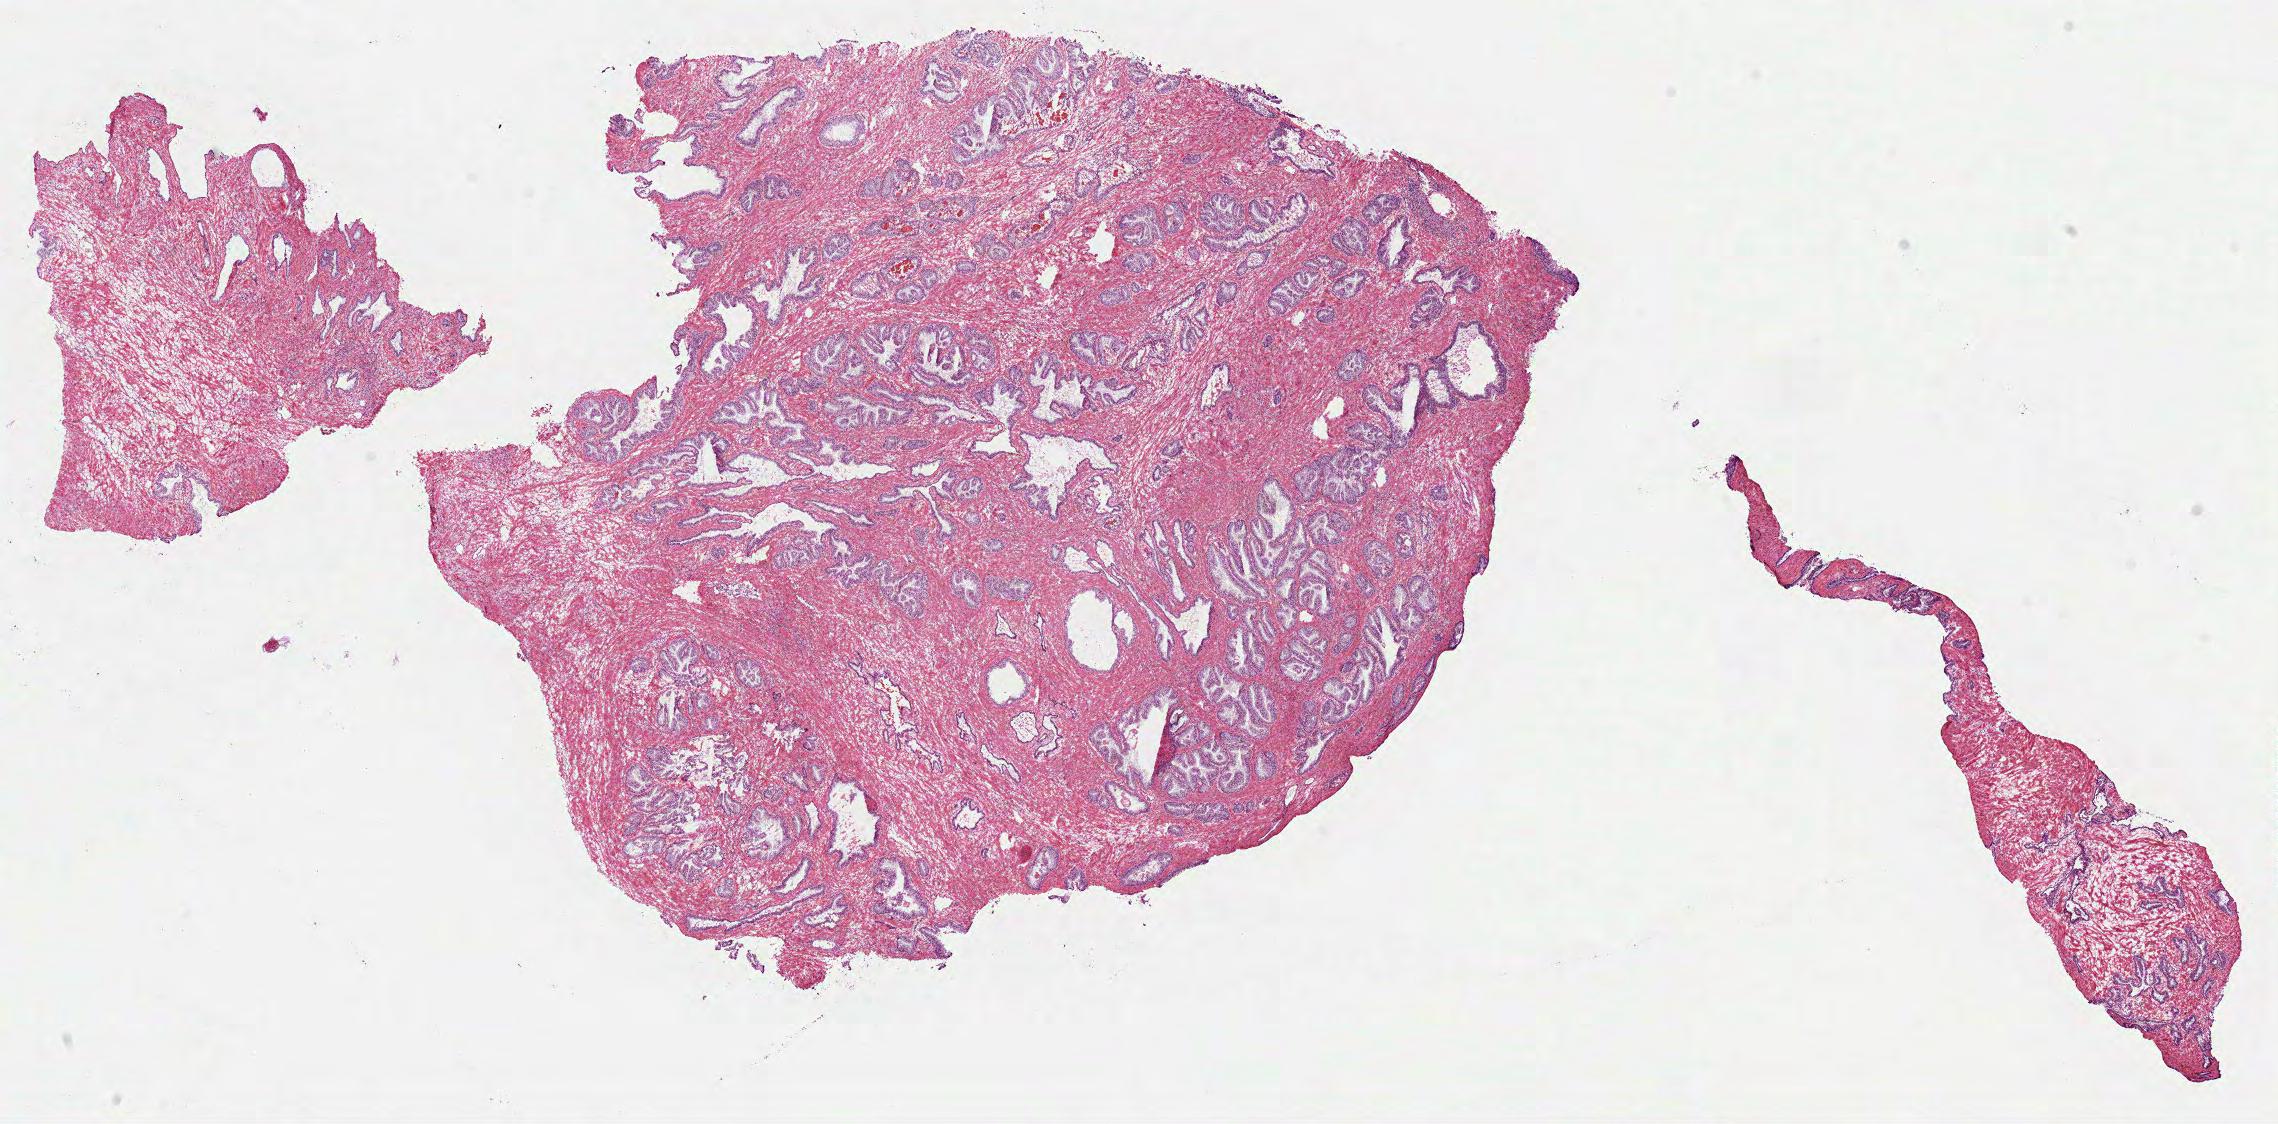
H&E-stained whole-slide image — whole scanned area (about 18.4 x 9.1 mm, from a 40x scan) shown as a low-resolution overview; frozen section; solid tissue normal (non-tumour tissue) sample from the prostate. Patient: male, age at initial diagnosis 44 years.
• this section: solid tissue normal sample (biorepository sample class)
• patient diagnosis: Acinar cell carcinoma (prostate gland)